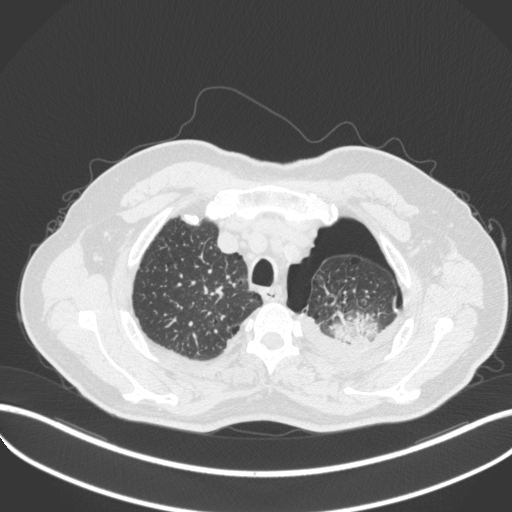
Chest CT, one axial slice; position 417 of 466 along the scan axis; 120 kVp; lung window (W 1500 / L -600 HU); 1 mm slice thickness; 512 × 512 image matrix, field of view 400 × 400 mm. Male patient, age 76 years. Case-level facts recorded for this patient, not image findings: clinical TNM (as recorded): T3 N0 M1b.
Structures marked on this image (rectangle marked by the reading radiologist):
- lung tumour (recorded histology: adenocarcinoma): bounding box <323,307,382,347> (left, top, right, bottom; pixels)